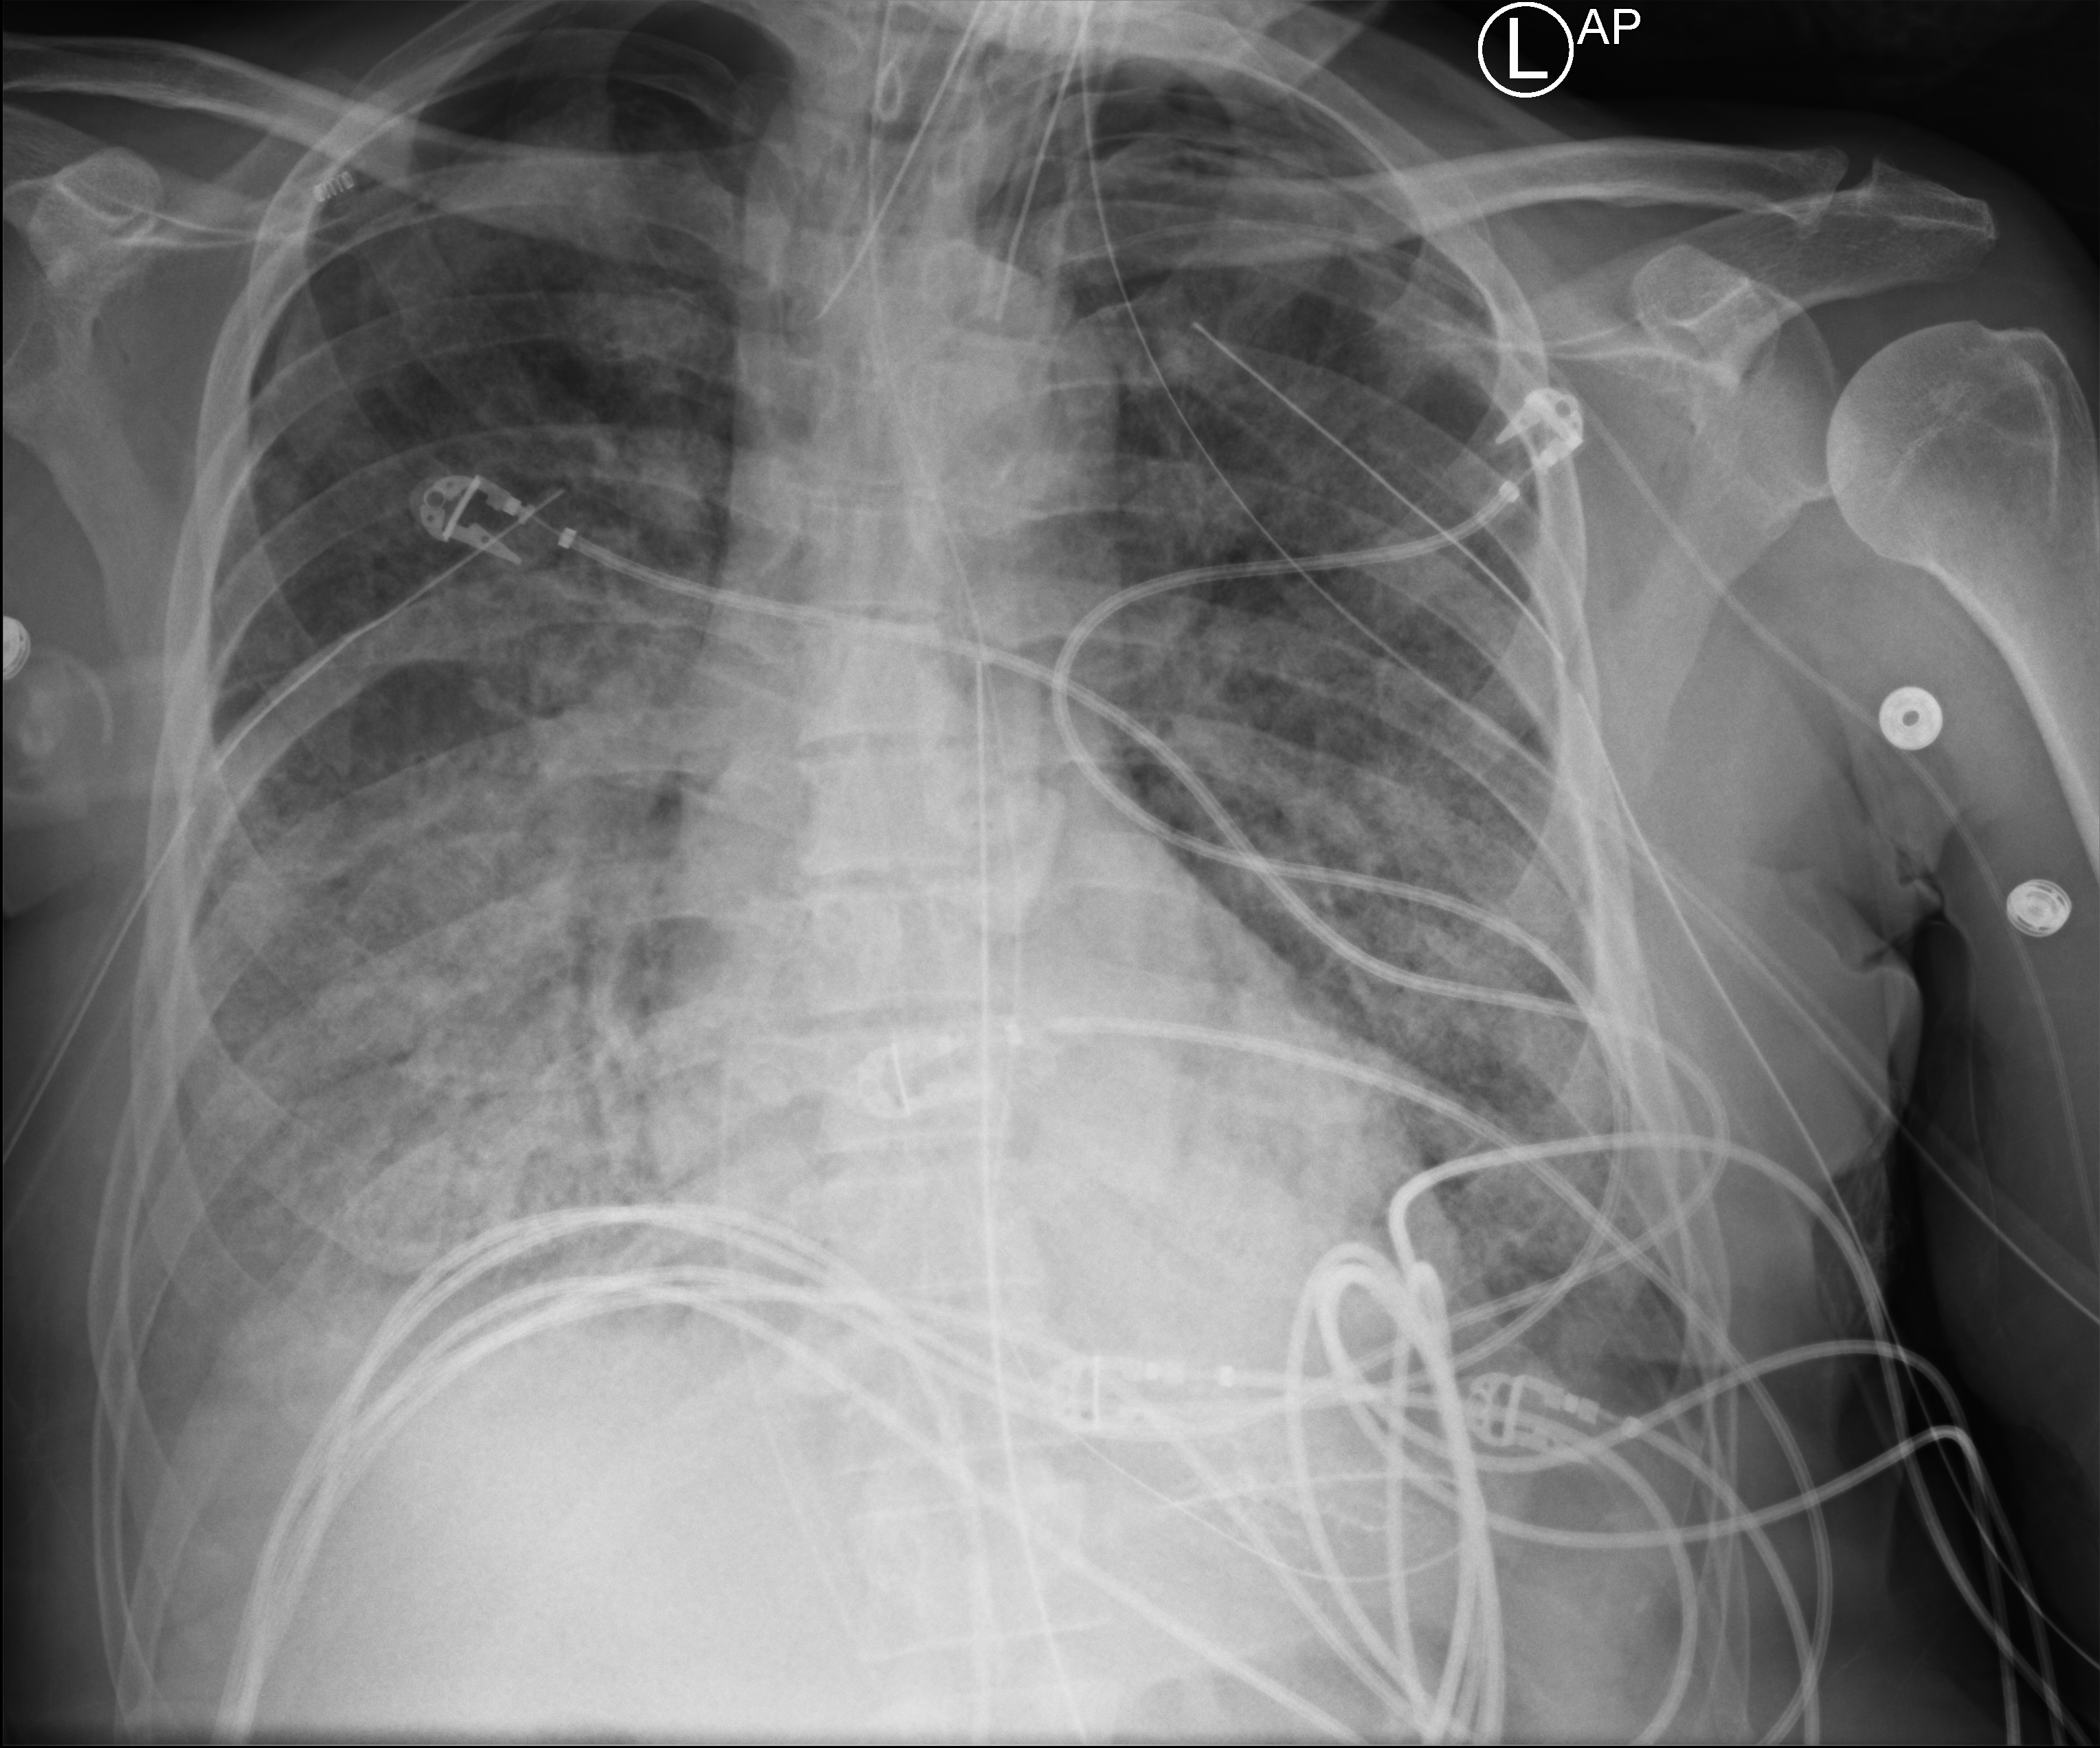
Bedside chest radiograph (computed radiography), anteroposterior (AP) projection. Male patient hospitalised with COVID-19, age 60–74 years.
Hospital-stay facts (about this admission, not read from this image; timing relative to this image not recorded): length of hospital stay: 31 days; smoking status (admission record): former; mechanically ventilated during this hospital stay: yes.